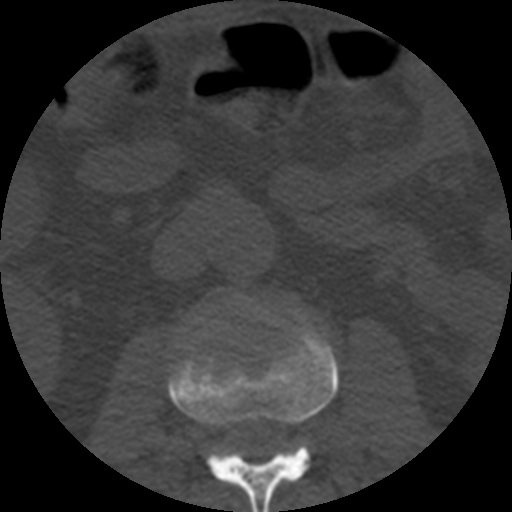
CT including the spine, one axial slice; slice 144 of 508 in the series (ordered by position); reconstruction kernel STANDARD; bone window (W 1800 / L 400 HU); 512 × 512 image matrix, field of view 160 × 160 mm. Patient age 57 years. From the clinical record (not read from this slice): primary cancer: prostate.
Annotated regions visible in this slice (semi-automatically segmented with operator editing):
- L2 vertebra: bounding box (x1, y1, x2, y2) in pixels: (167, 317, 338, 512)